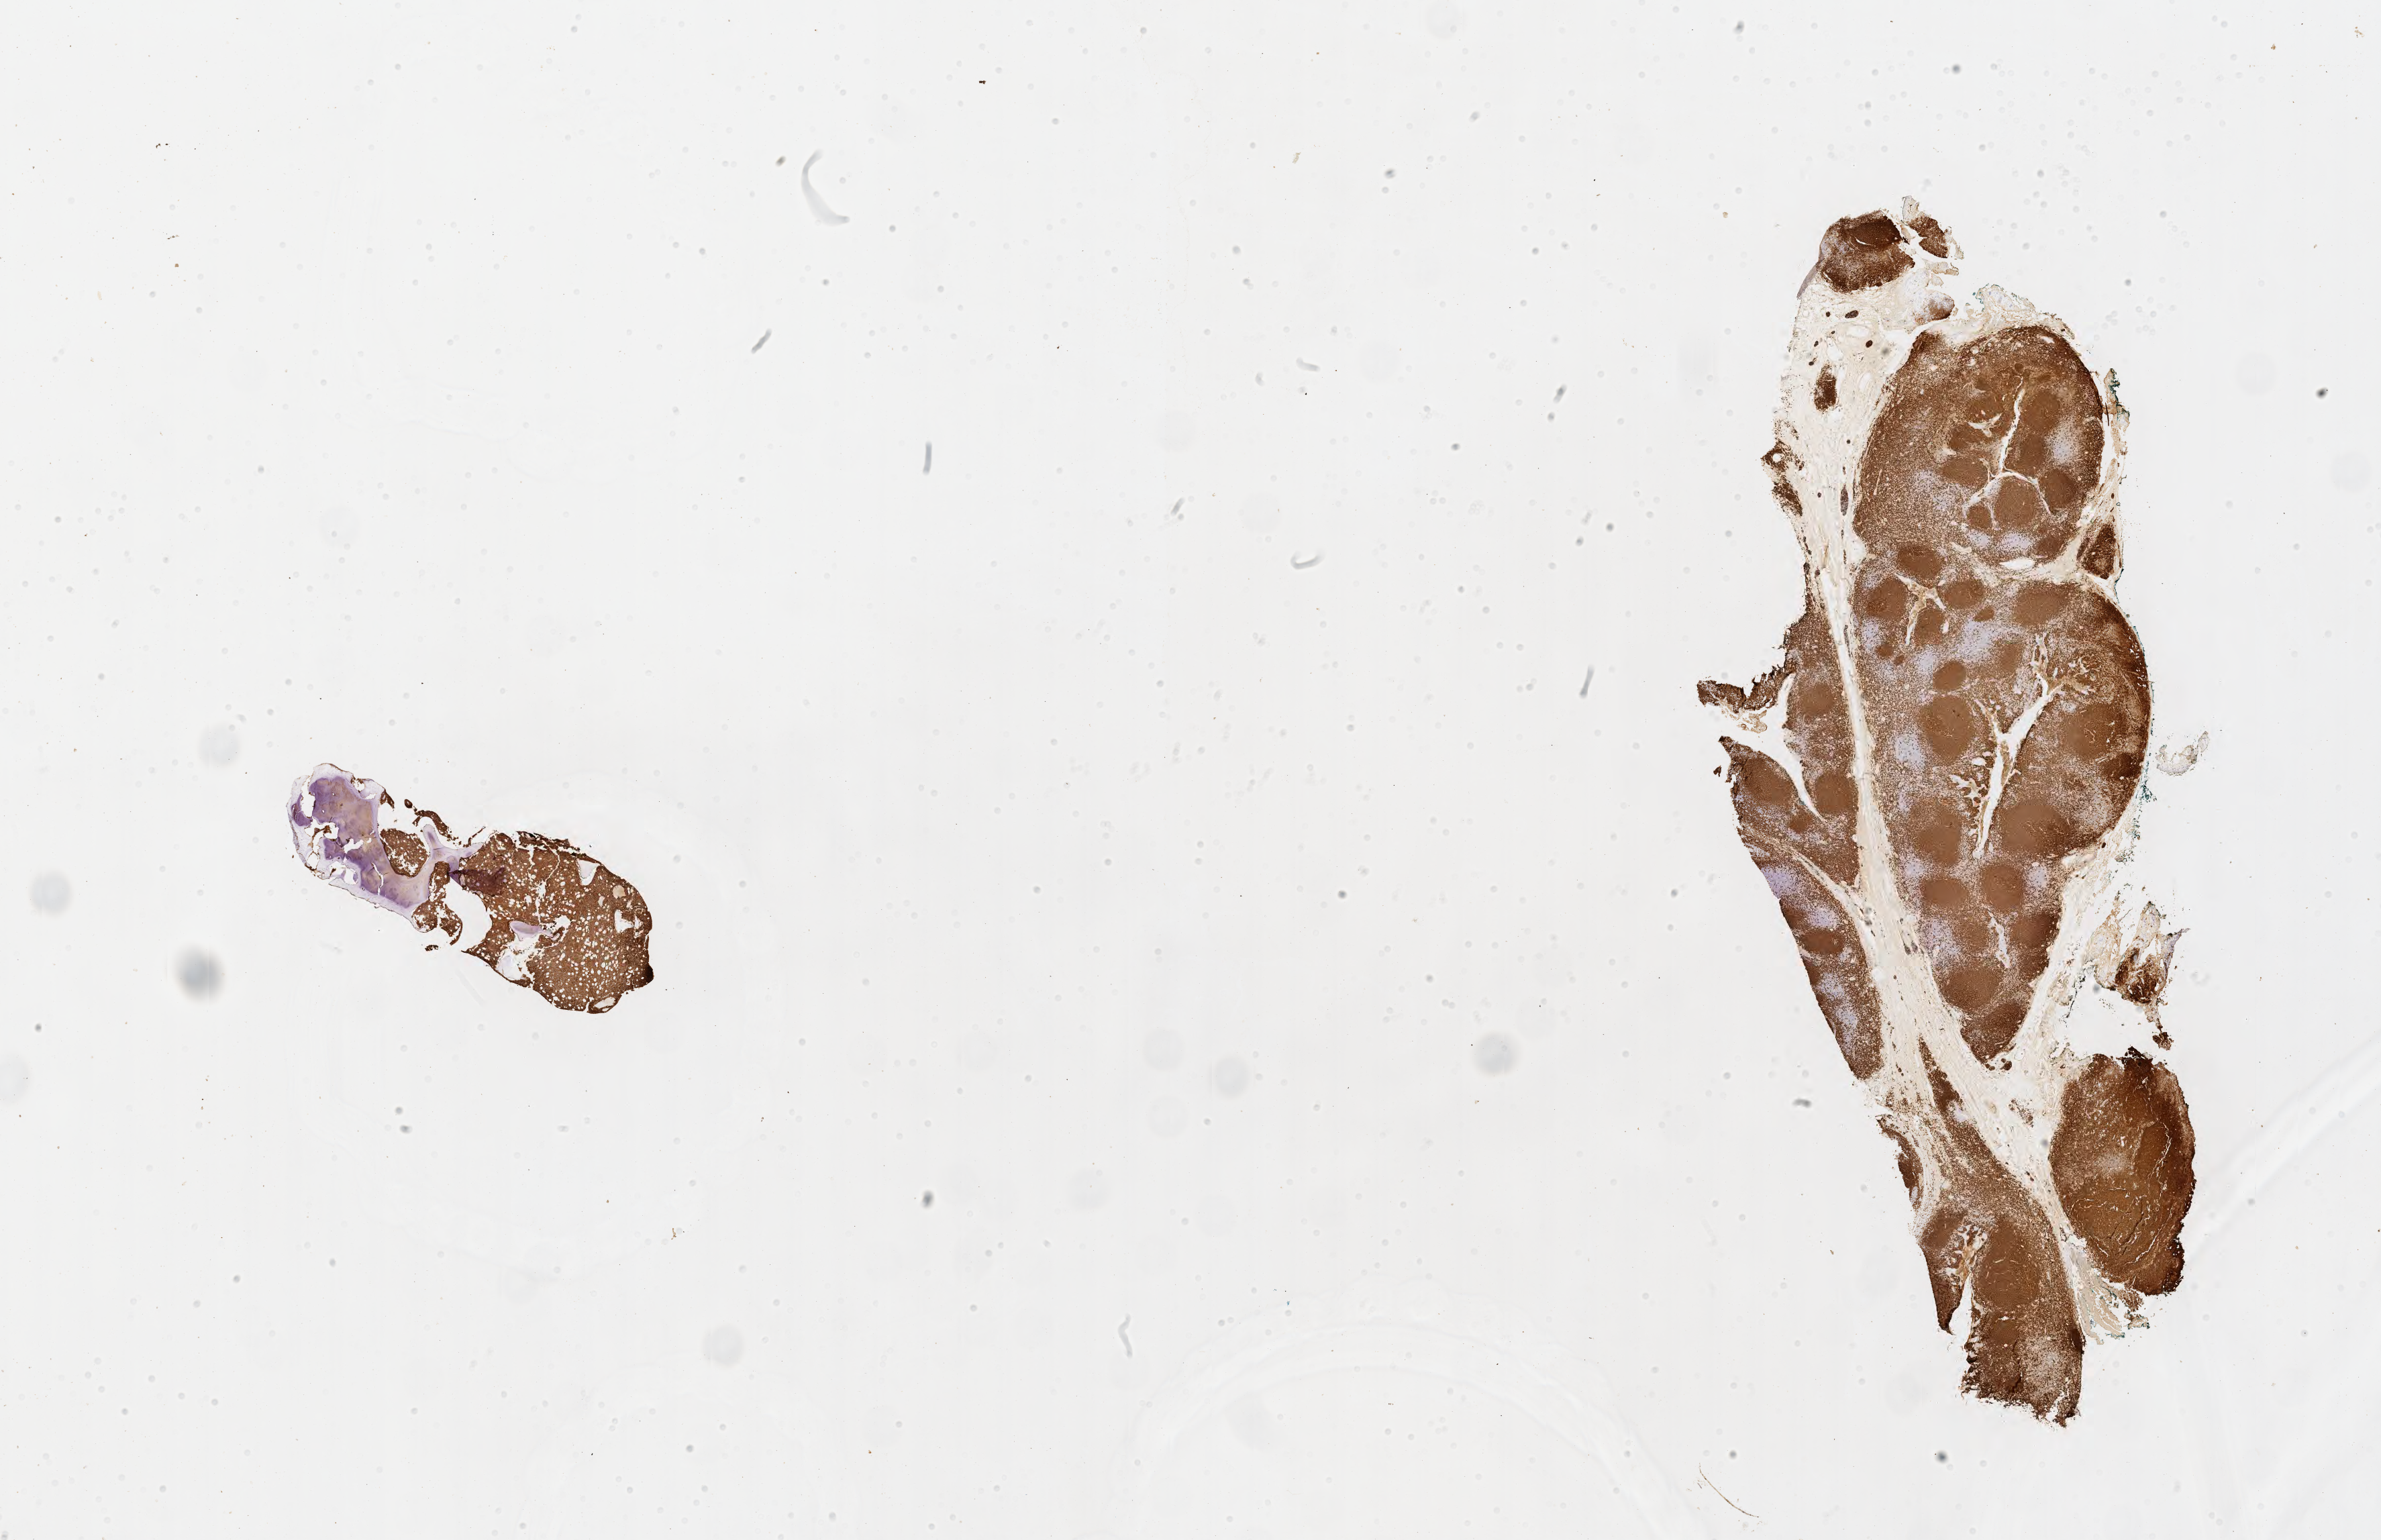
Whole-slide image, immunohistochemical stain for CD20 — shown as a low-resolution overview of the whole scanned area (about 28.7 x 18.5 mm), tumor tissue, site: bone marrow. Patient: male, 15 years old.
Histologic diagnosis: Burkitt lymphoma, NOS.